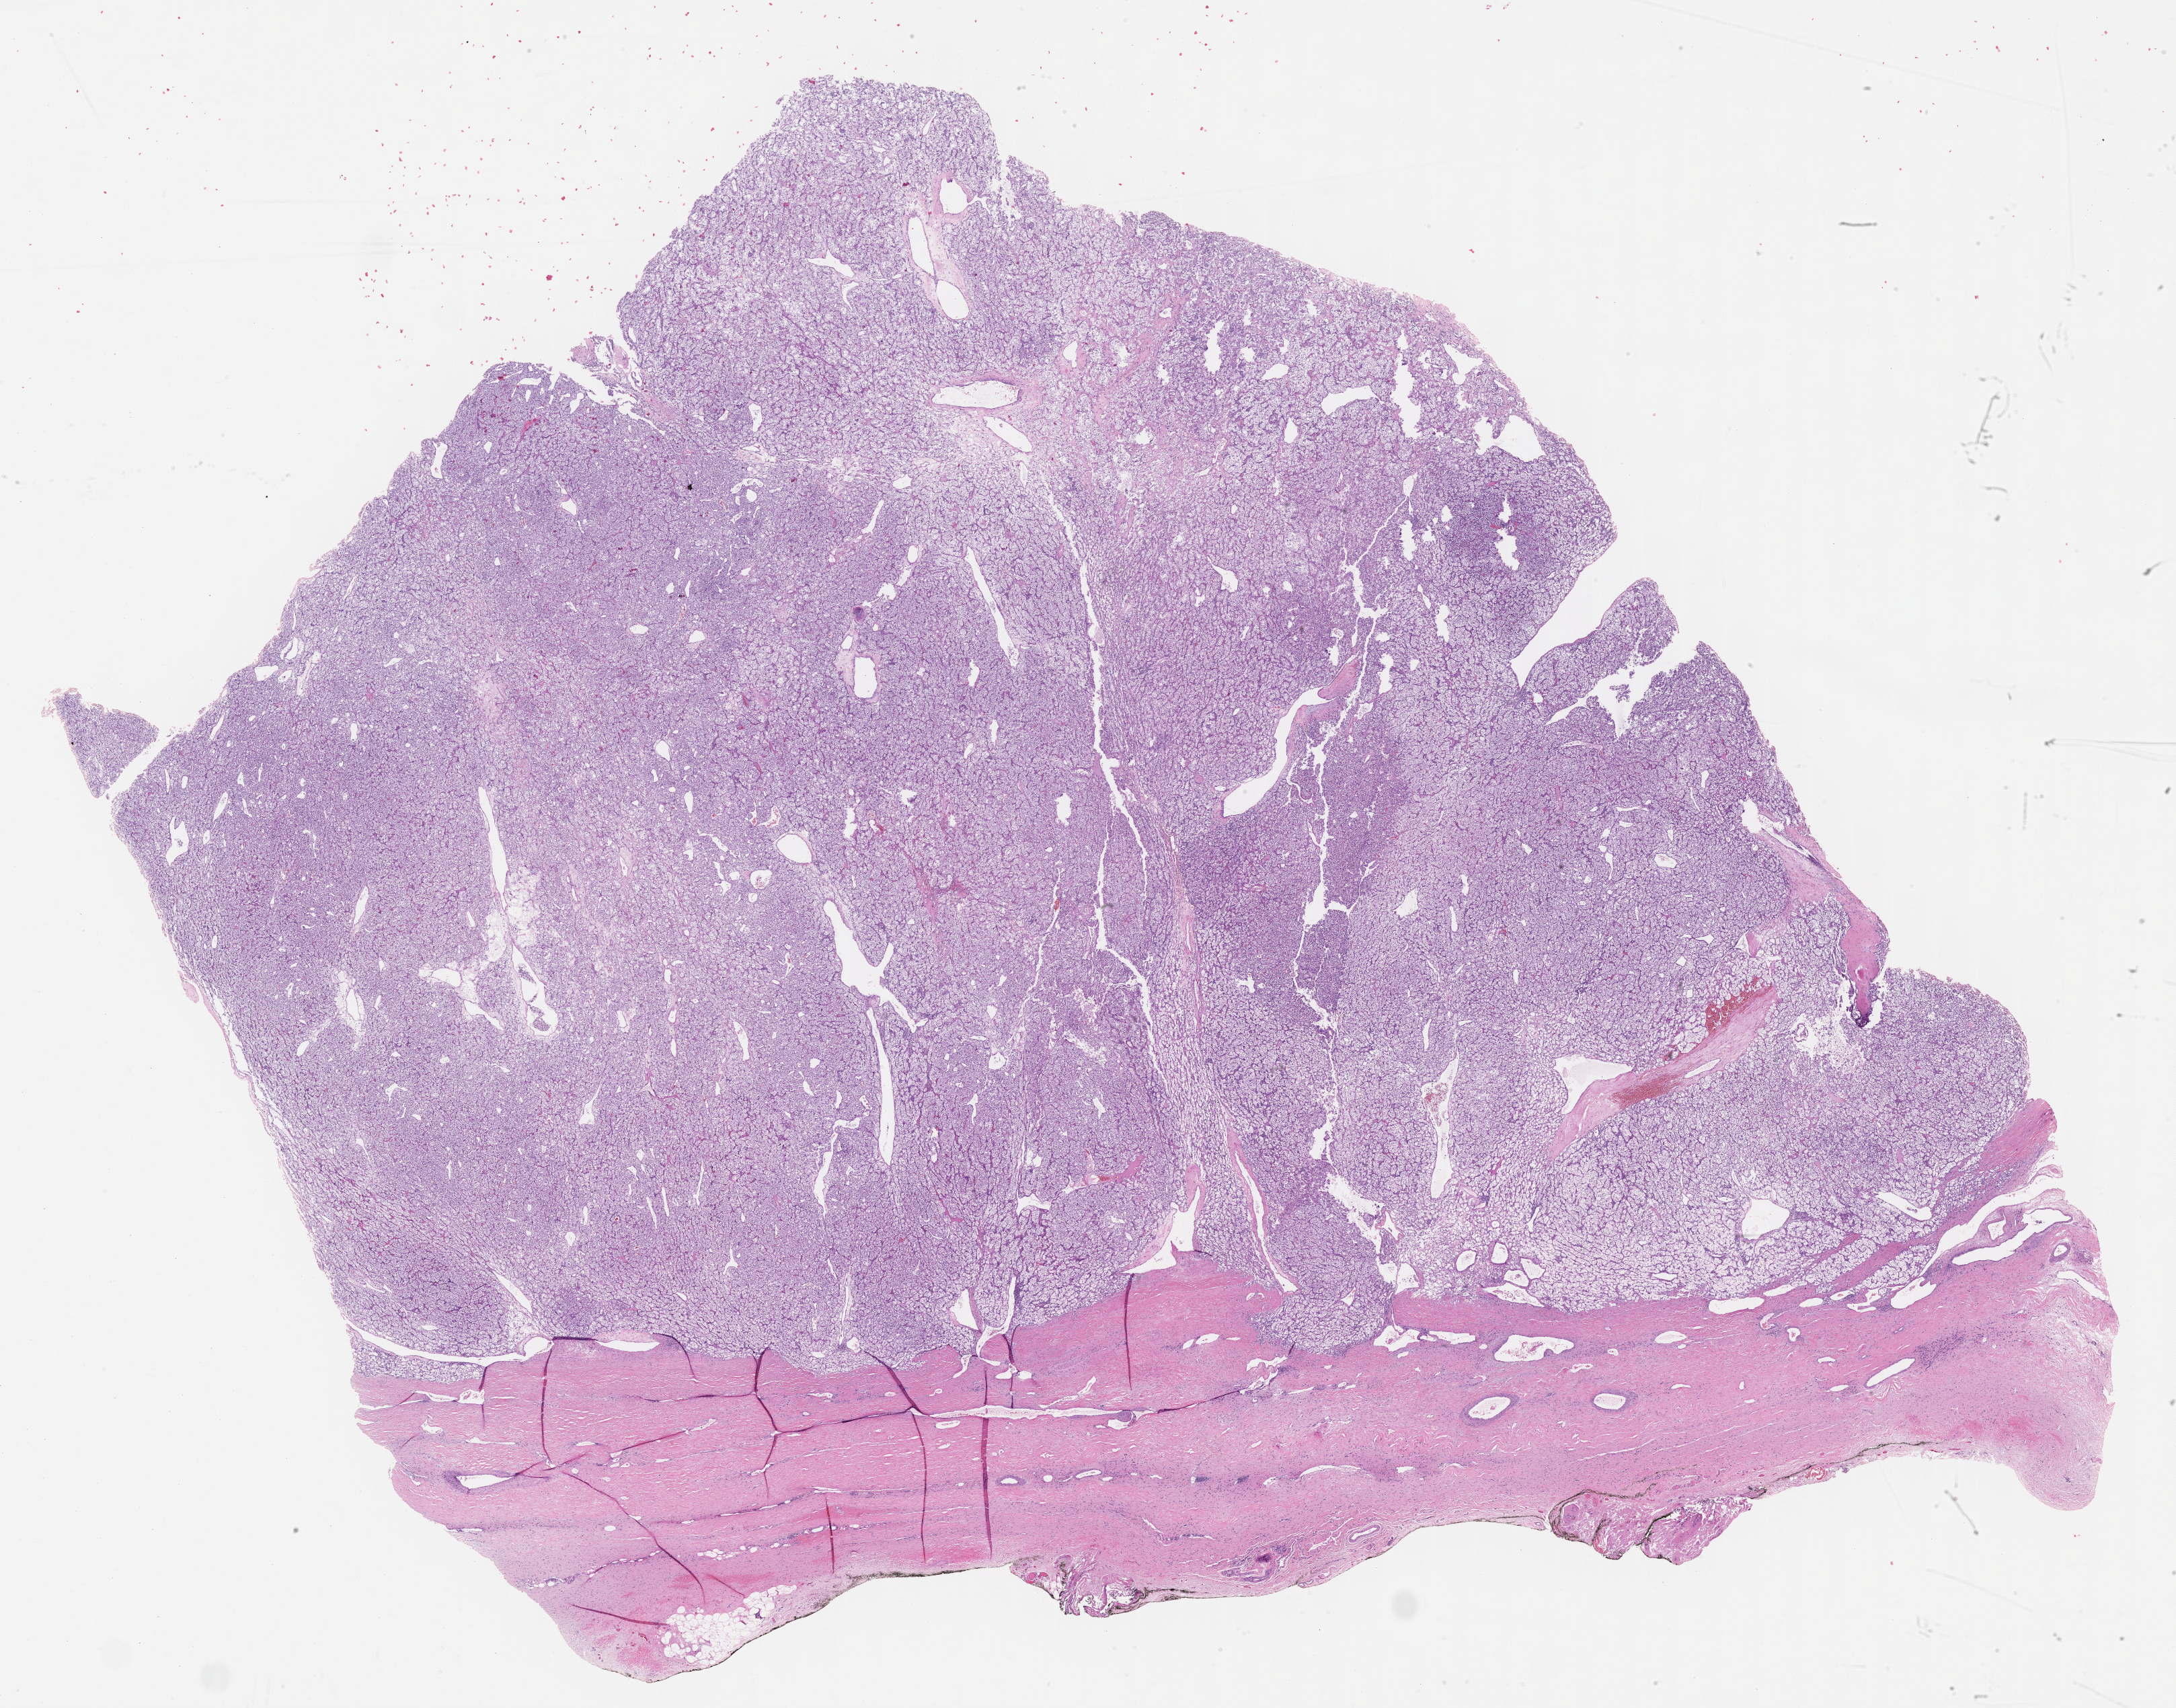
Hematoxylin and eosin (H&E) stained whole-slide image, low-resolution overview of the scanned area, about 26.2 x 20.5 mm (acquisition: 40x scan). Formalin-fixed paraffin-embedded (FFPE) diagnostic section. Kidney, primary tumour sample. Female patient; age at initial diagnosis 69 years. Histologic grade: G3 (poorly differentiated).
TNM: T3a NX M0. Pathologic diagnosis: Clear cell adenocarcinoma, NOS. AJCC pathologic stage: III.